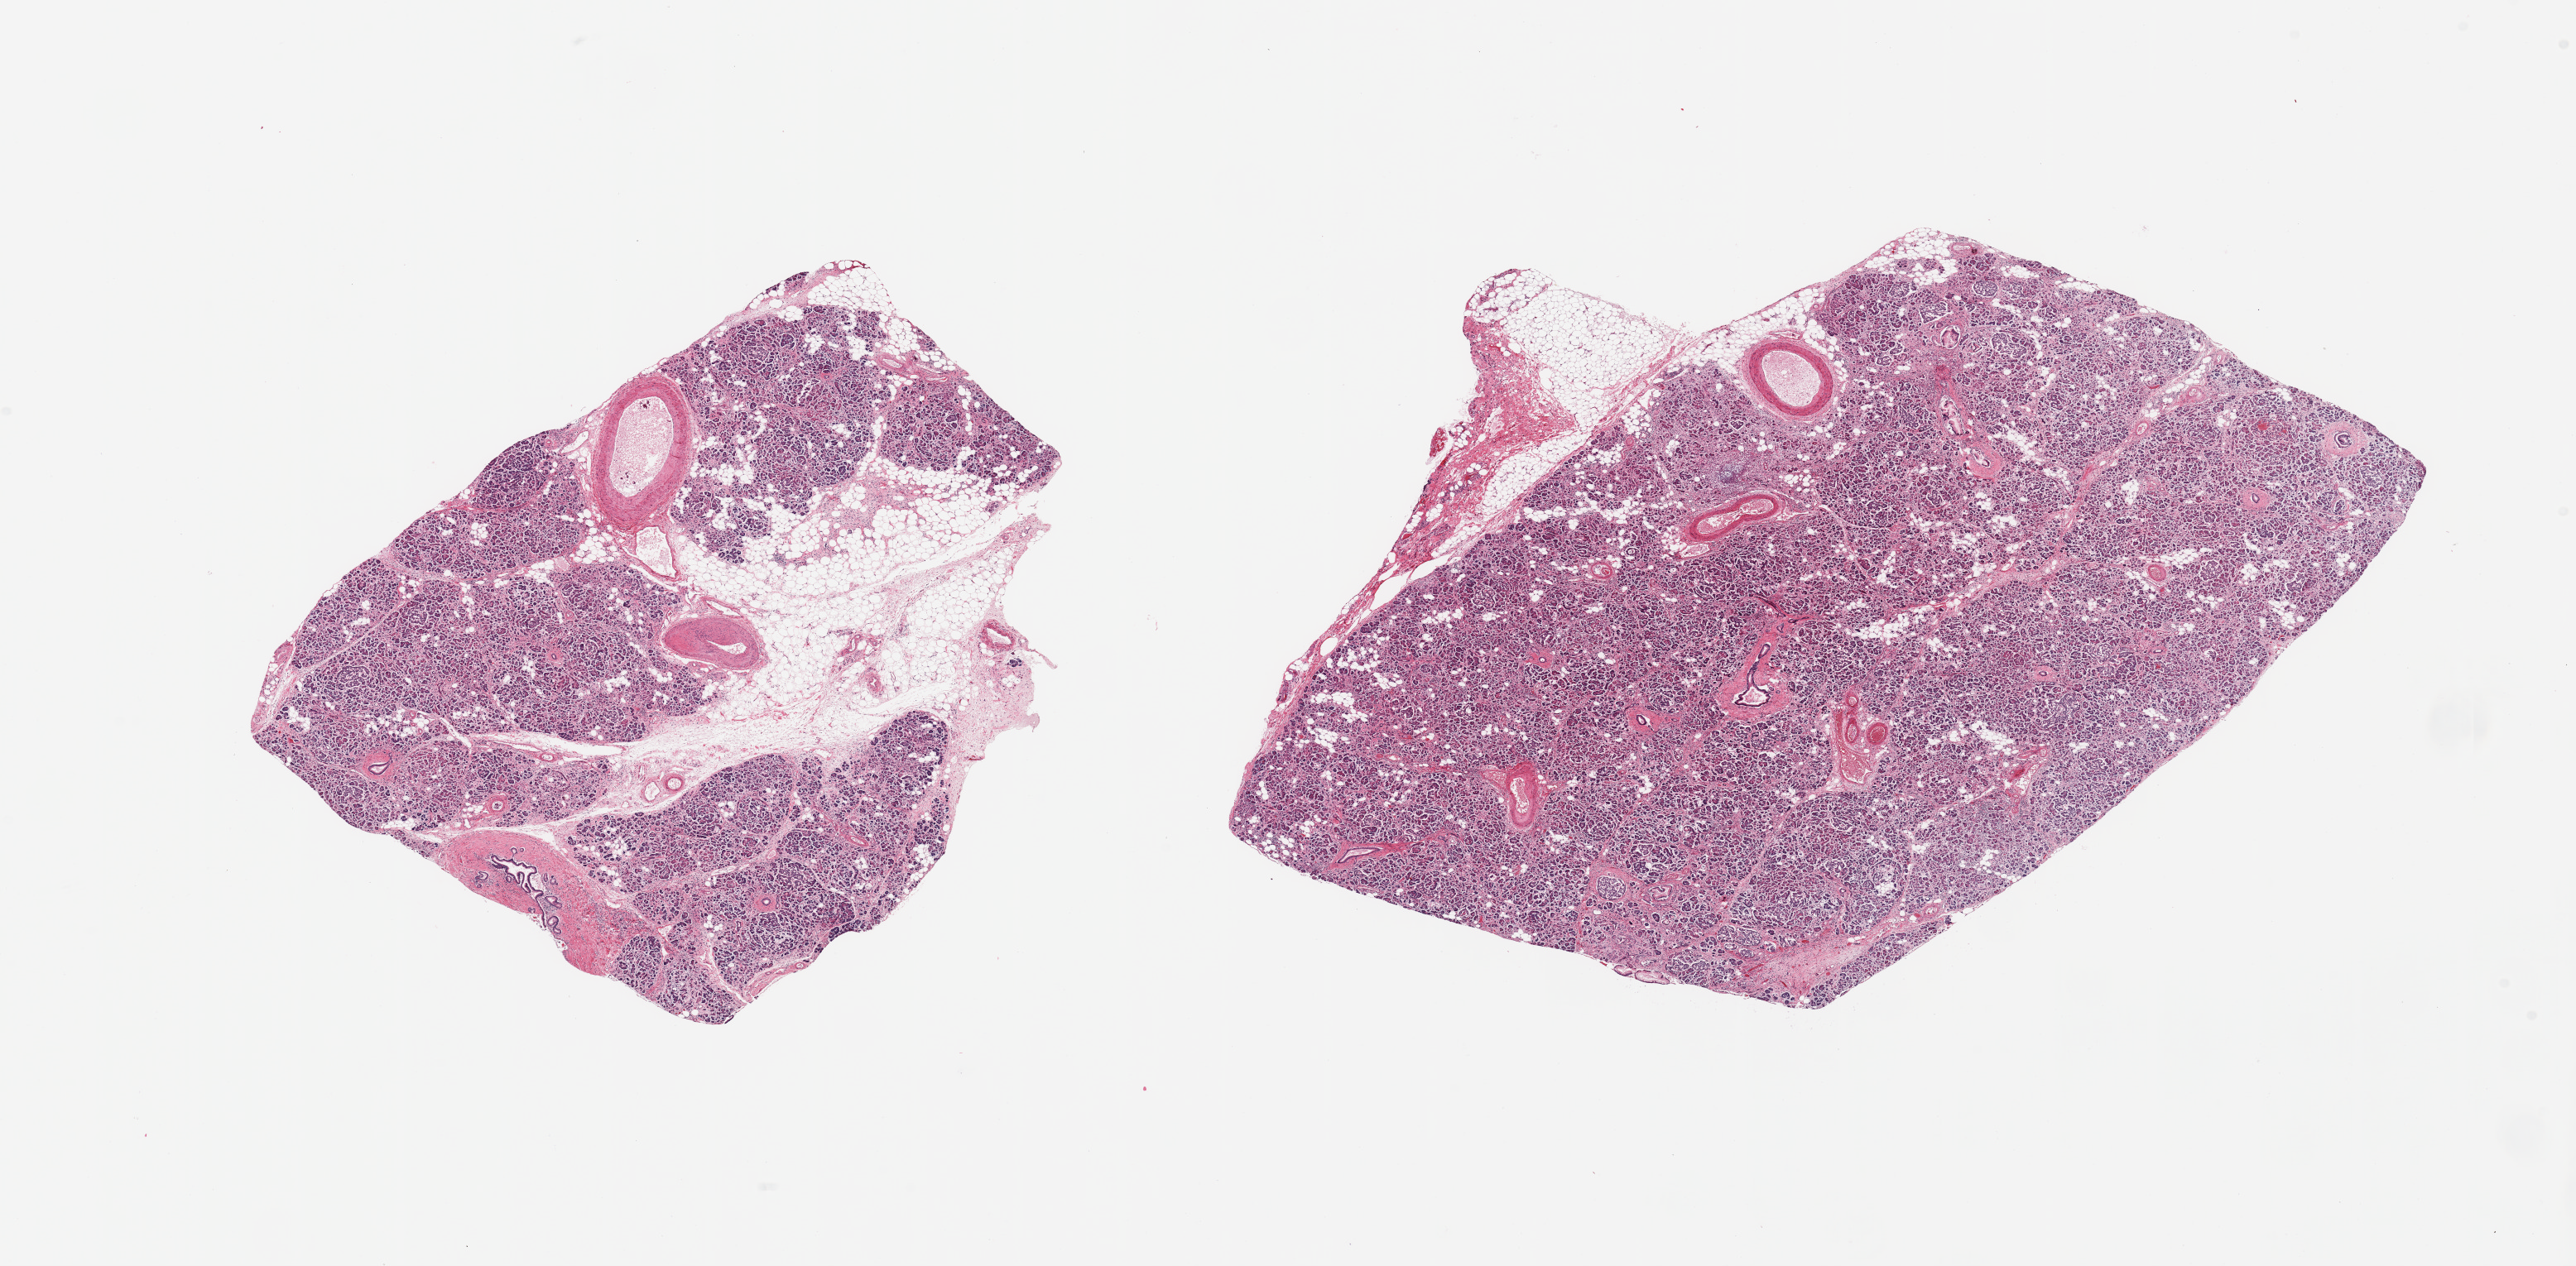
Hematoxylin and eosin (H&E) whole-slide image, whole scanned area (about 24.6 x 12.1 mm, slide scanned at 20x) shown as a low-resolution overview; PAXgene-fixed paraffin-embedded (PFPE) section; target tissue: pancreas; donor tissue sample. Donor sex: male.
* reviewer comment on this tissue sample: 2 pieces; 30% and 10% external/internal fat; periductal and interstitial fibrosis with acinar atrophy; islets observed, some chronic inflammation, focal PanIN 1A